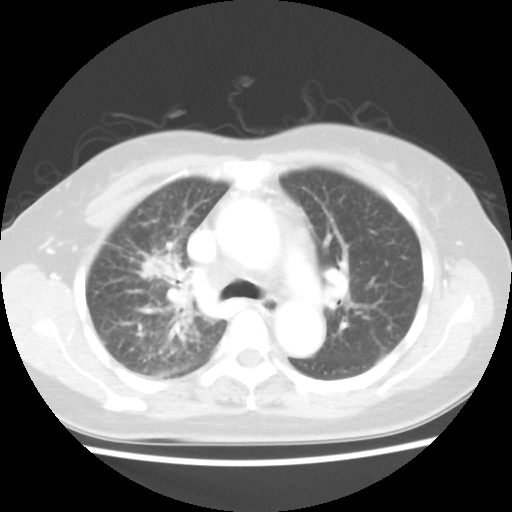
Chest CT, one axial slice; position 30 of 48 along the scan axis; reconstruction kernel STANDARD; lung window (W 1500 / L -600 HU); 5 mm slice thickness; 512 × 512 image matrix, field of view 312 × 312 mm. Female patient, age 55 years. From the clinical record (not read from this slice): clinical TNM (as recorded): T1b N3 M1a.
Outlined on this slice (rectangle marked by the reading radiologist):
- lung tumour (recorded histology: adenocarcinoma): bounding box [x1, y1, x2, y2] px = [143, 257, 185, 281]